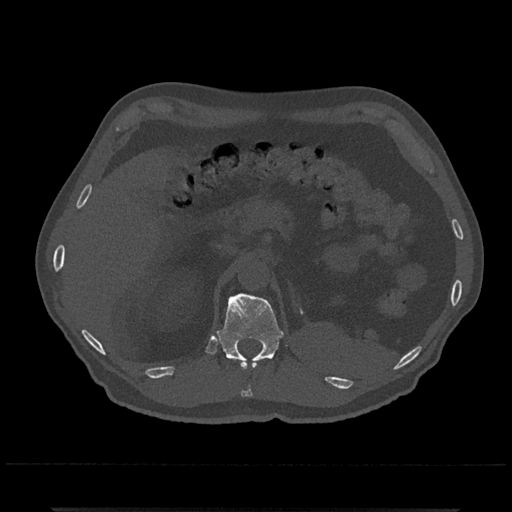
CT including the spine, one axial slice; reconstruction kernel Br40s/3; bone window (W 1800 / L 400 HU); 512 × 512 image matrix, field of view 393 × 393 mm. Male patient, age 67 years. Case-level facts recorded for this patient, not image findings: primary cancer: prostate.
Annotated regions visible in this slice (semi-automatic segmentation, software-assisted and operator-edited):
- T11 vertebra: bounding box <230,358,257,397> (left, top, right, bottom; pixels)
- T12 vertebra: <217,293,284,367>